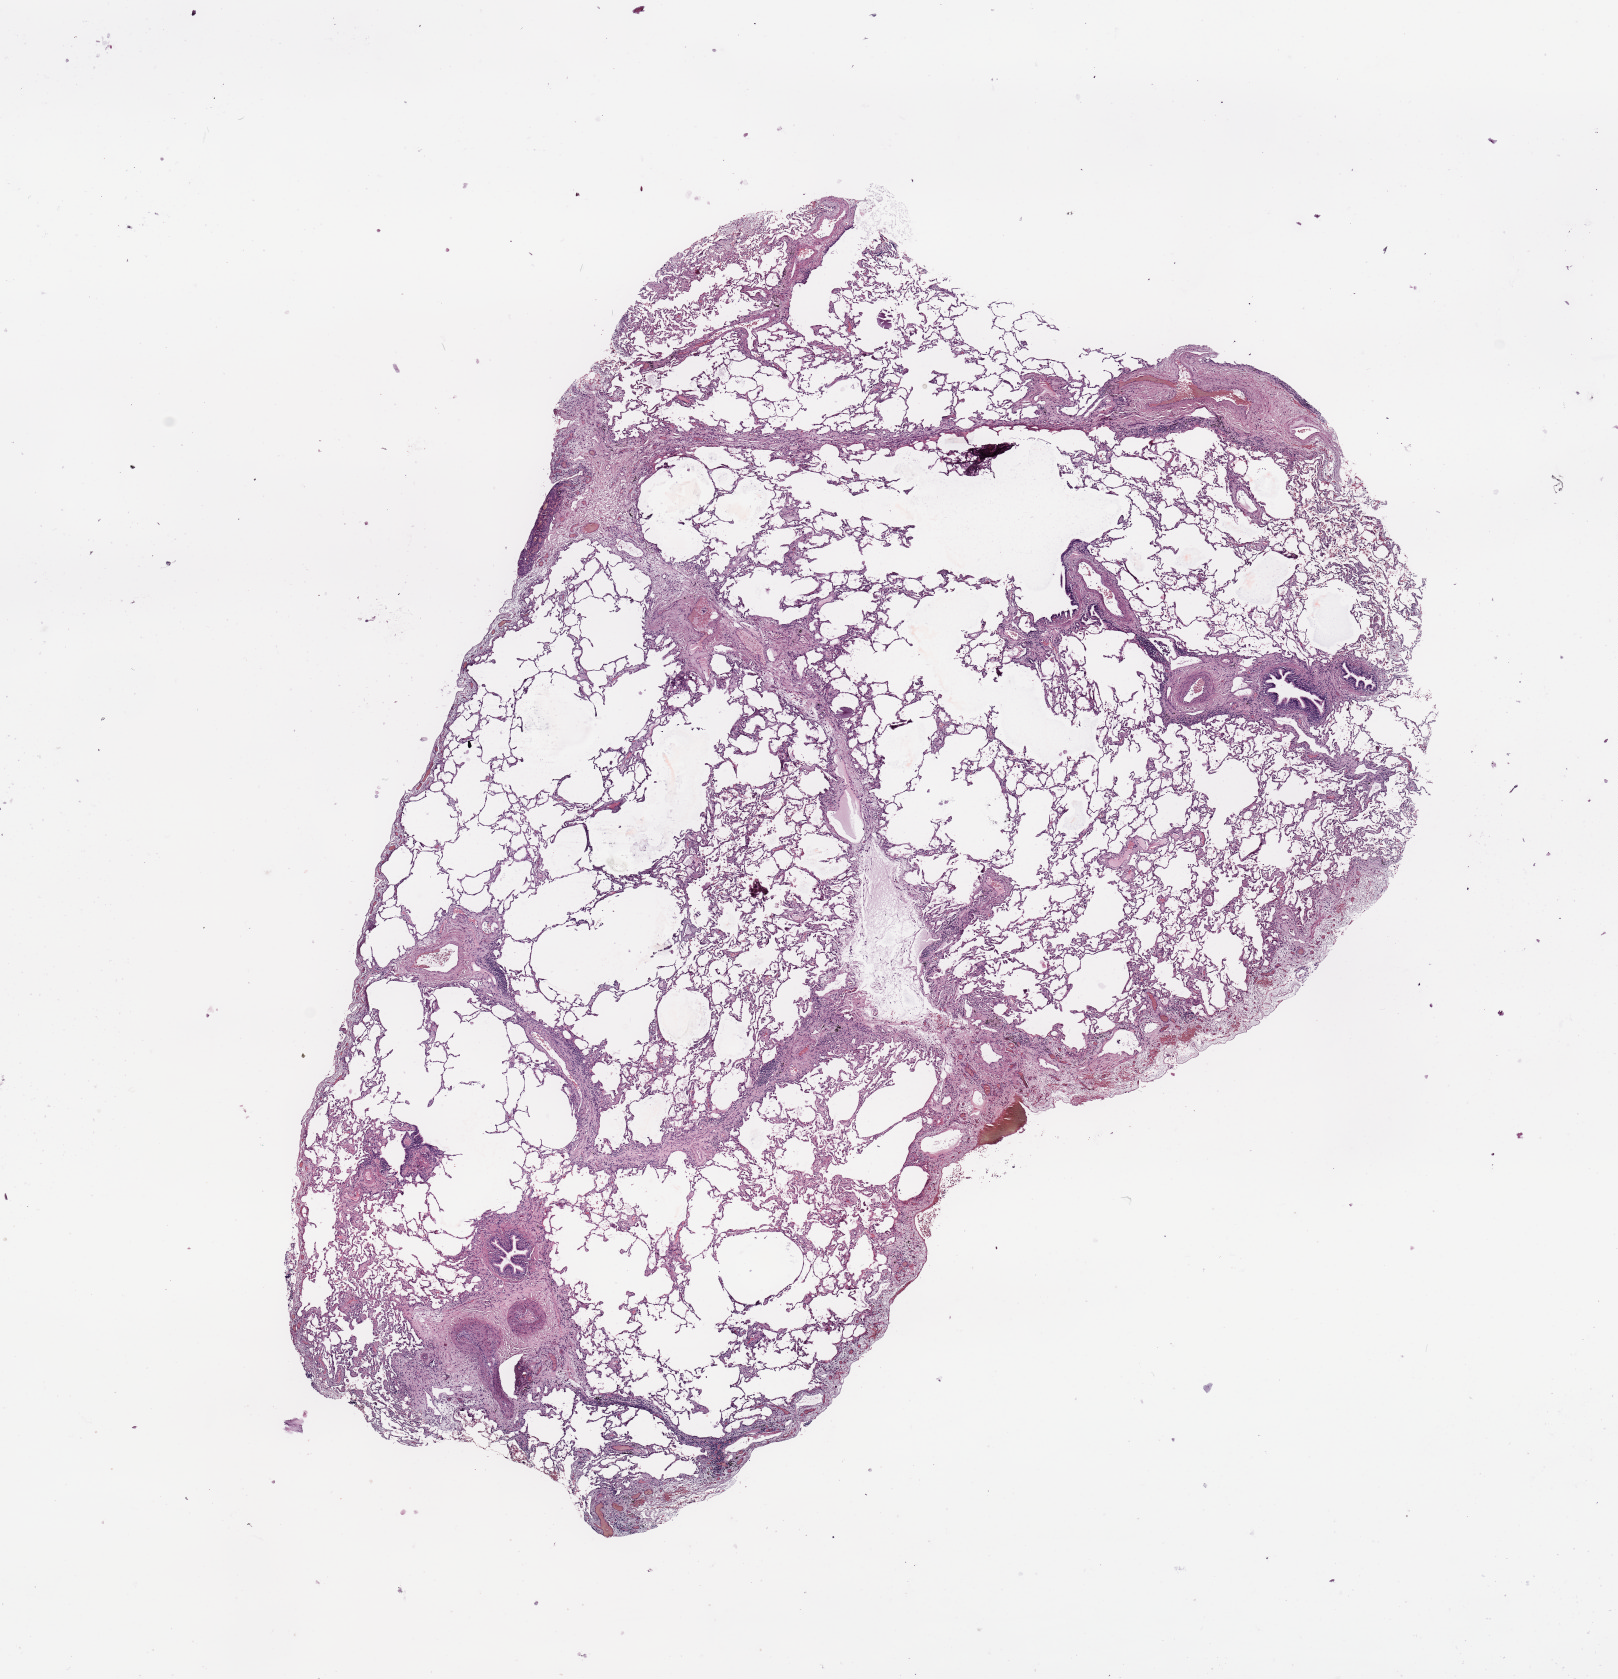
H&E whole-slide image — shown as a low-resolution overview of the whole scanned area (about 12.8 x 13.3 mm, slide scanned at 20x). Normal (non-tumour) tissue sample, sampled site: lung. Patient: female, age 70 years.
This section: normal (non-tumour) tissue from the same patient. Patient diagnosis: Squamous cell carcinoma, NOS.